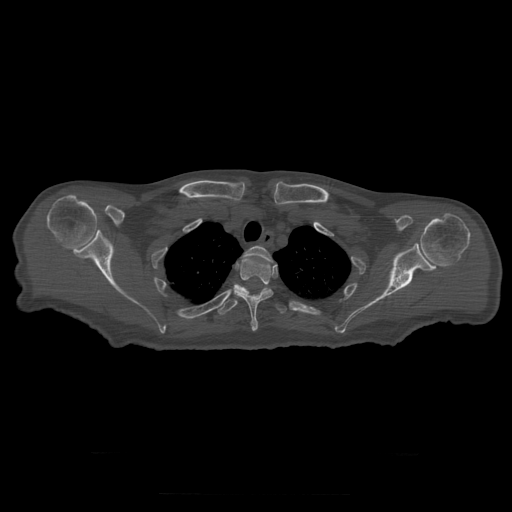
CT including the spine, one axial slice; 120 kVp; bone window (W 1800 / L 400 HU); 1.25 mm slice thickness; 512 × 512 image matrix, field of view 510 × 510 mm. Patient age 73 years. From the clinical record (not read from this slice): primary cancer: prostate.
Outlined on this slice (semi-automatic segmentation, software-assisted and operator-edited):
- T2 vertebra: bounding box <243,246,276,266> (left, top, right, bottom; pixels)
- T3 vertebra: <234,257,274,332>
- T4 vertebra: <218,288,287,315>